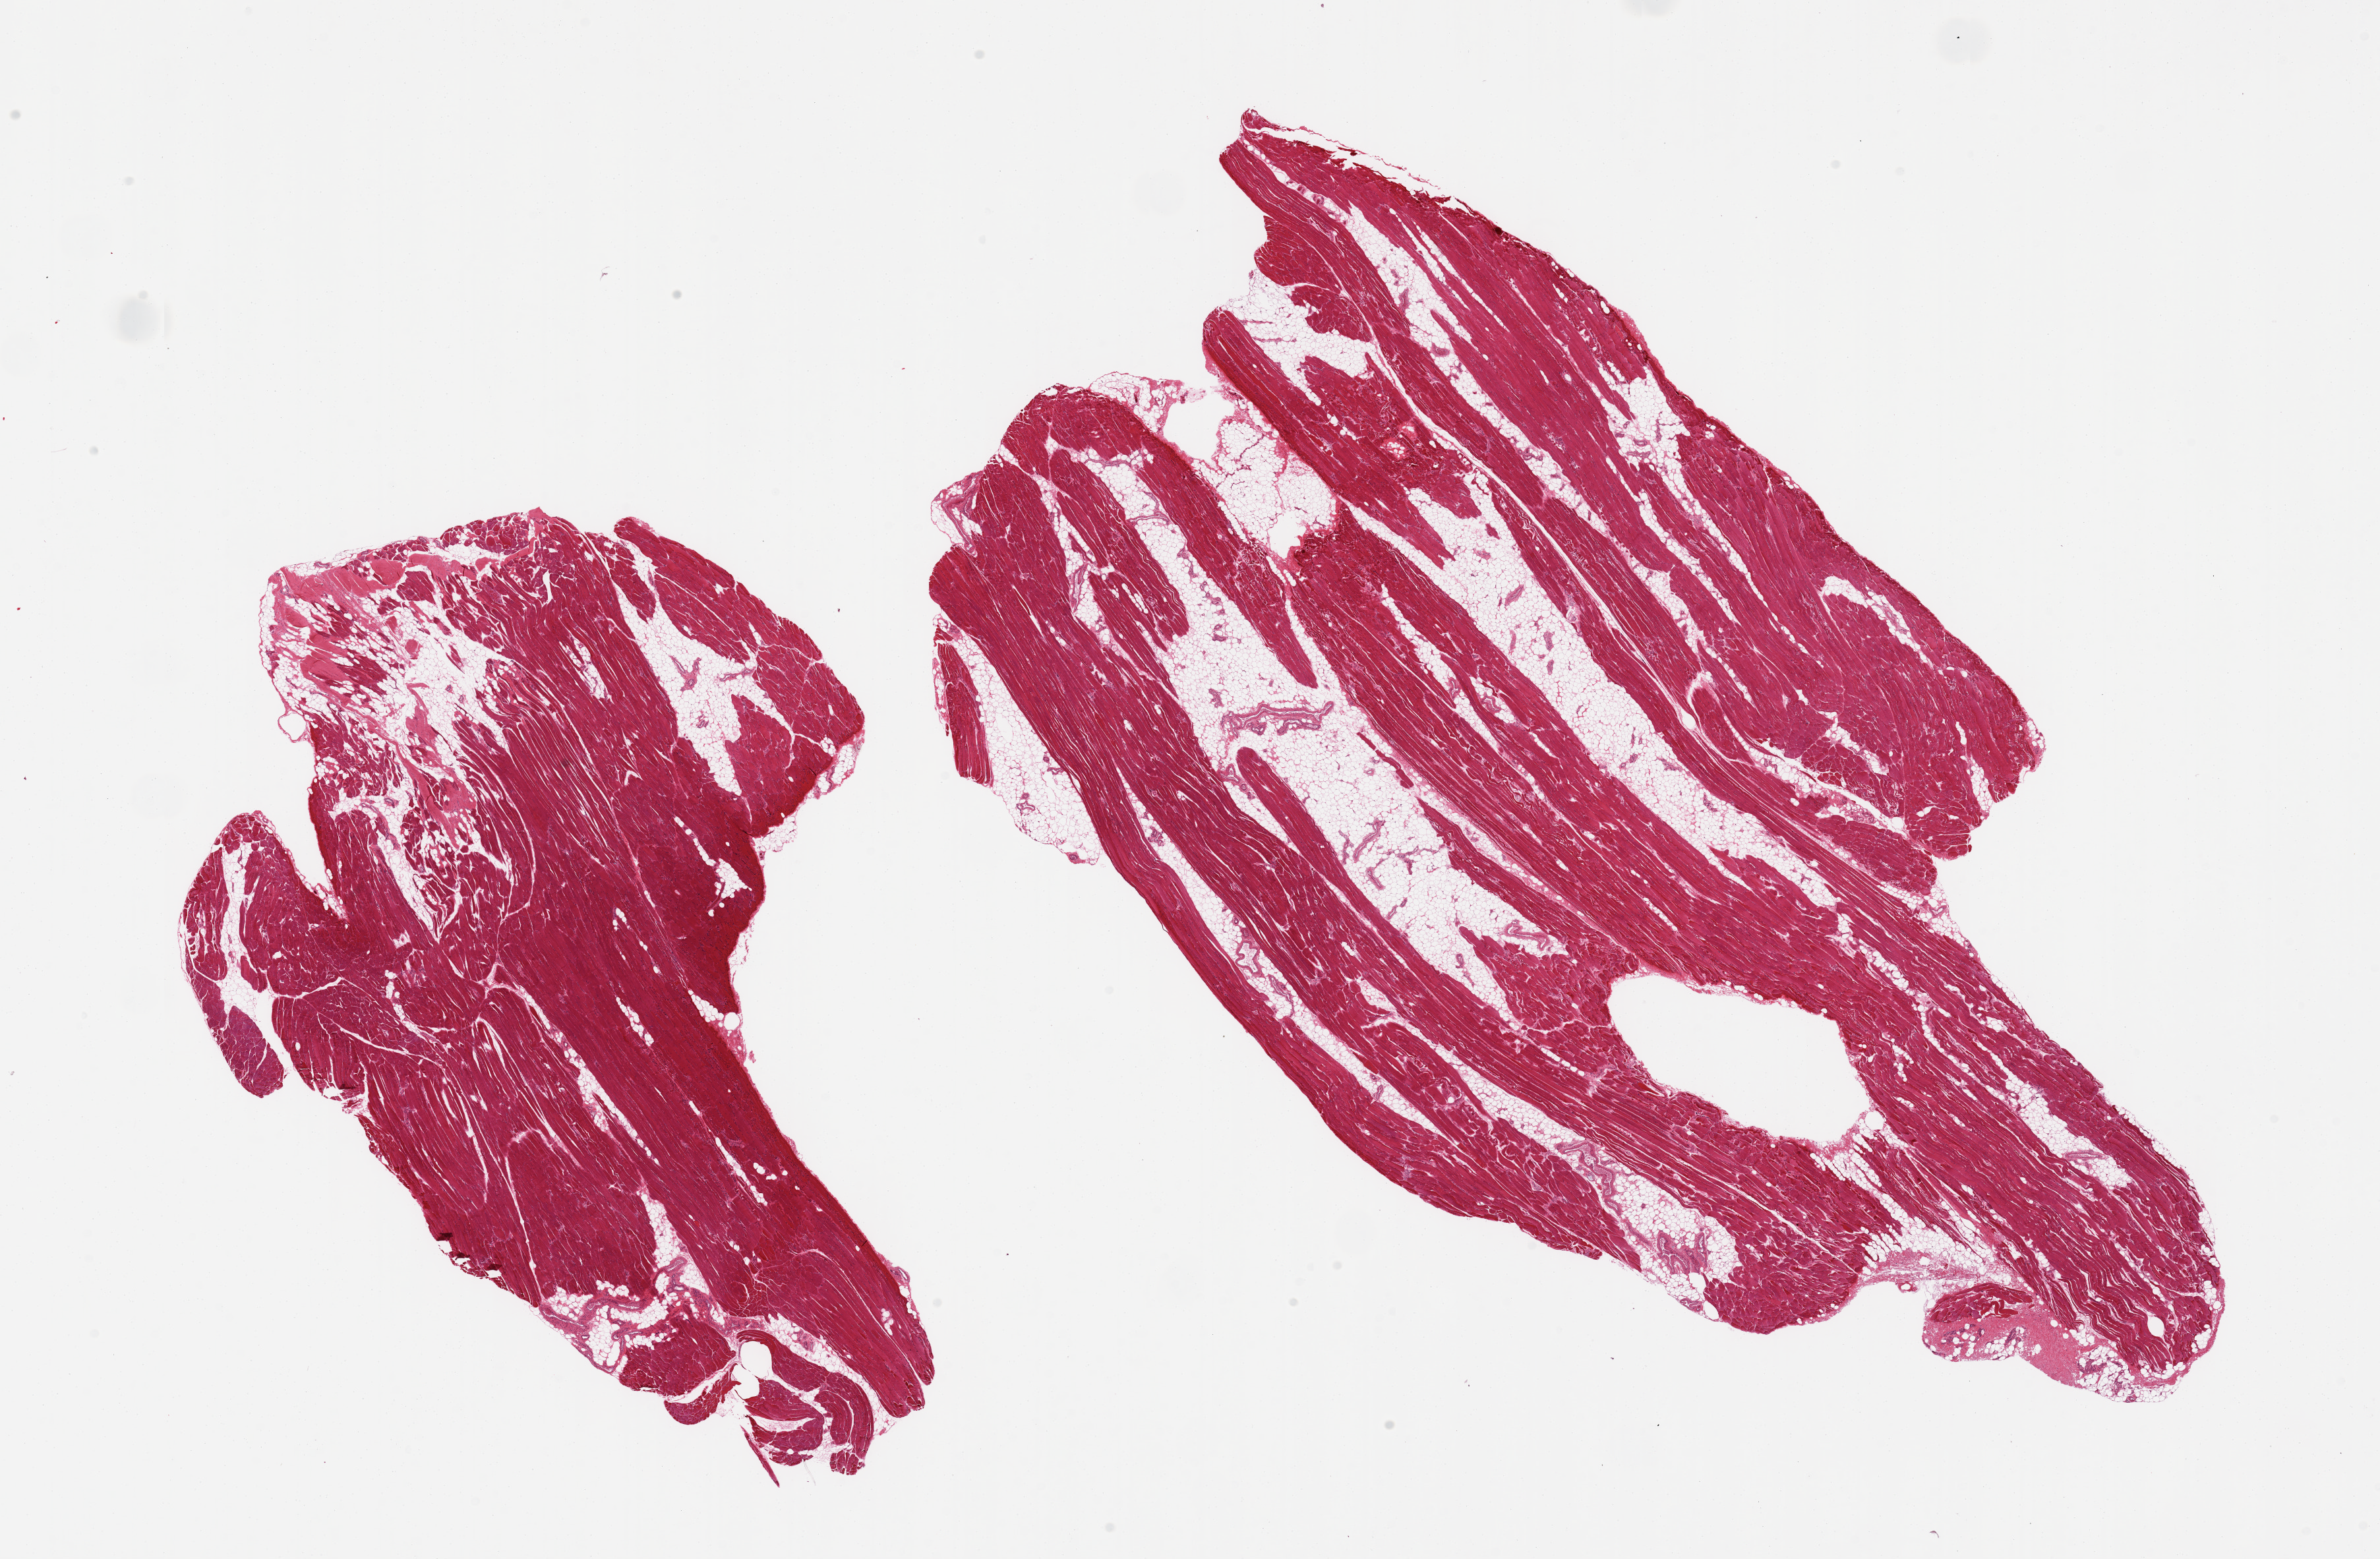
Whole-slide image, hematoxylin and eosin (H&E) stain — shown as a low-resolution overview of the whole scanned area (about 28.5 x 18.7 mm, from a 20x scan); PAXgene-fixed paraffin-embedded (PFPE) section; target tissue: skeletal muscle; donor tissue sample. Male donor.
Reviewer comment on this tissue sample: 2 pieces ~30% interstitial fat.